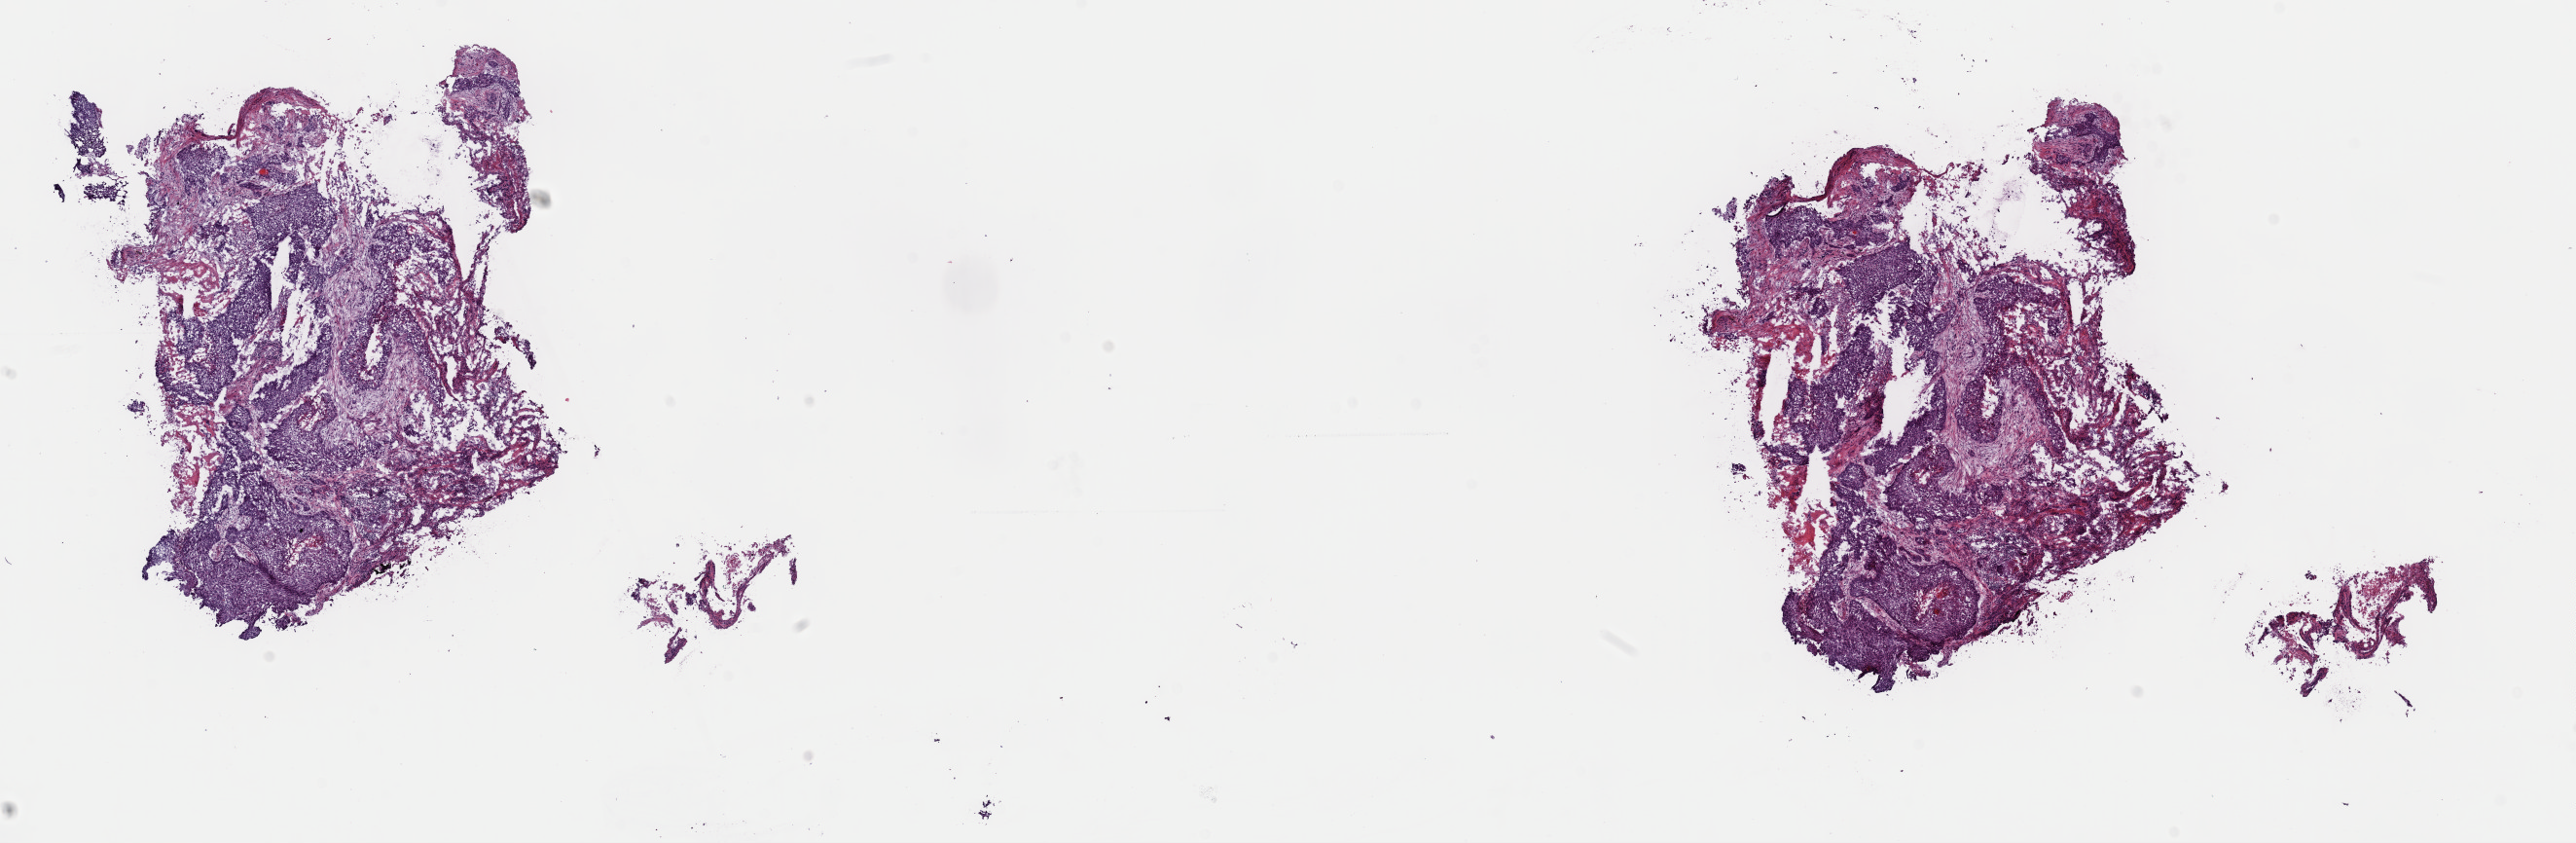
H&E whole-slide image — shown as a low-resolution overview of the whole scanned area (about 20.9 x 6.8 mm, slide scanned at 40x). Frozen section. Sample: primary tumour, lung. Male patient; age at initial diagnosis 63 years. Slide review estimates, as recorded: tumour cells 70%, tumour nuclei 70%, normal cells 0%, stromal cells 25%, necrosis 5%. Inflammatory infiltration, as recorded: lymphocyte infiltration 2%, monocyte infiltration 1%, neutrophil infiltration 3%.
• AJCC pathologic stage: IIB (7th edition)
• diagnosis: Squamous cell carcinoma, NOS (upper lobe, lung)
• laterality: left